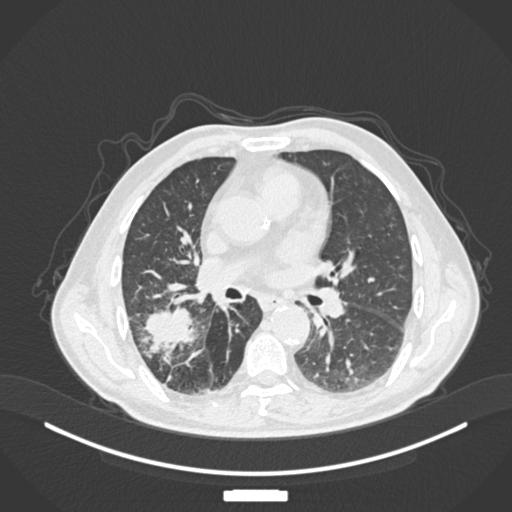
Chest CT, one axial slice. 120 kVp. Lung window (W 1500 / L -600 HU). 1 mm slice thickness. 512 × 512 image matrix, field of view 400 × 400 mm. Male patient, age 72 years. From the clinical record (not read from this slice): clinical TNM (as recorded): T3 N2 M0.
Structures marked on this image (bounding box drawn by a radiologist):
- lung tumour (recorded histology: adenocarcinoma): bounding box (x1, y1, x2, y2) in pixels: (140, 303, 199, 356)